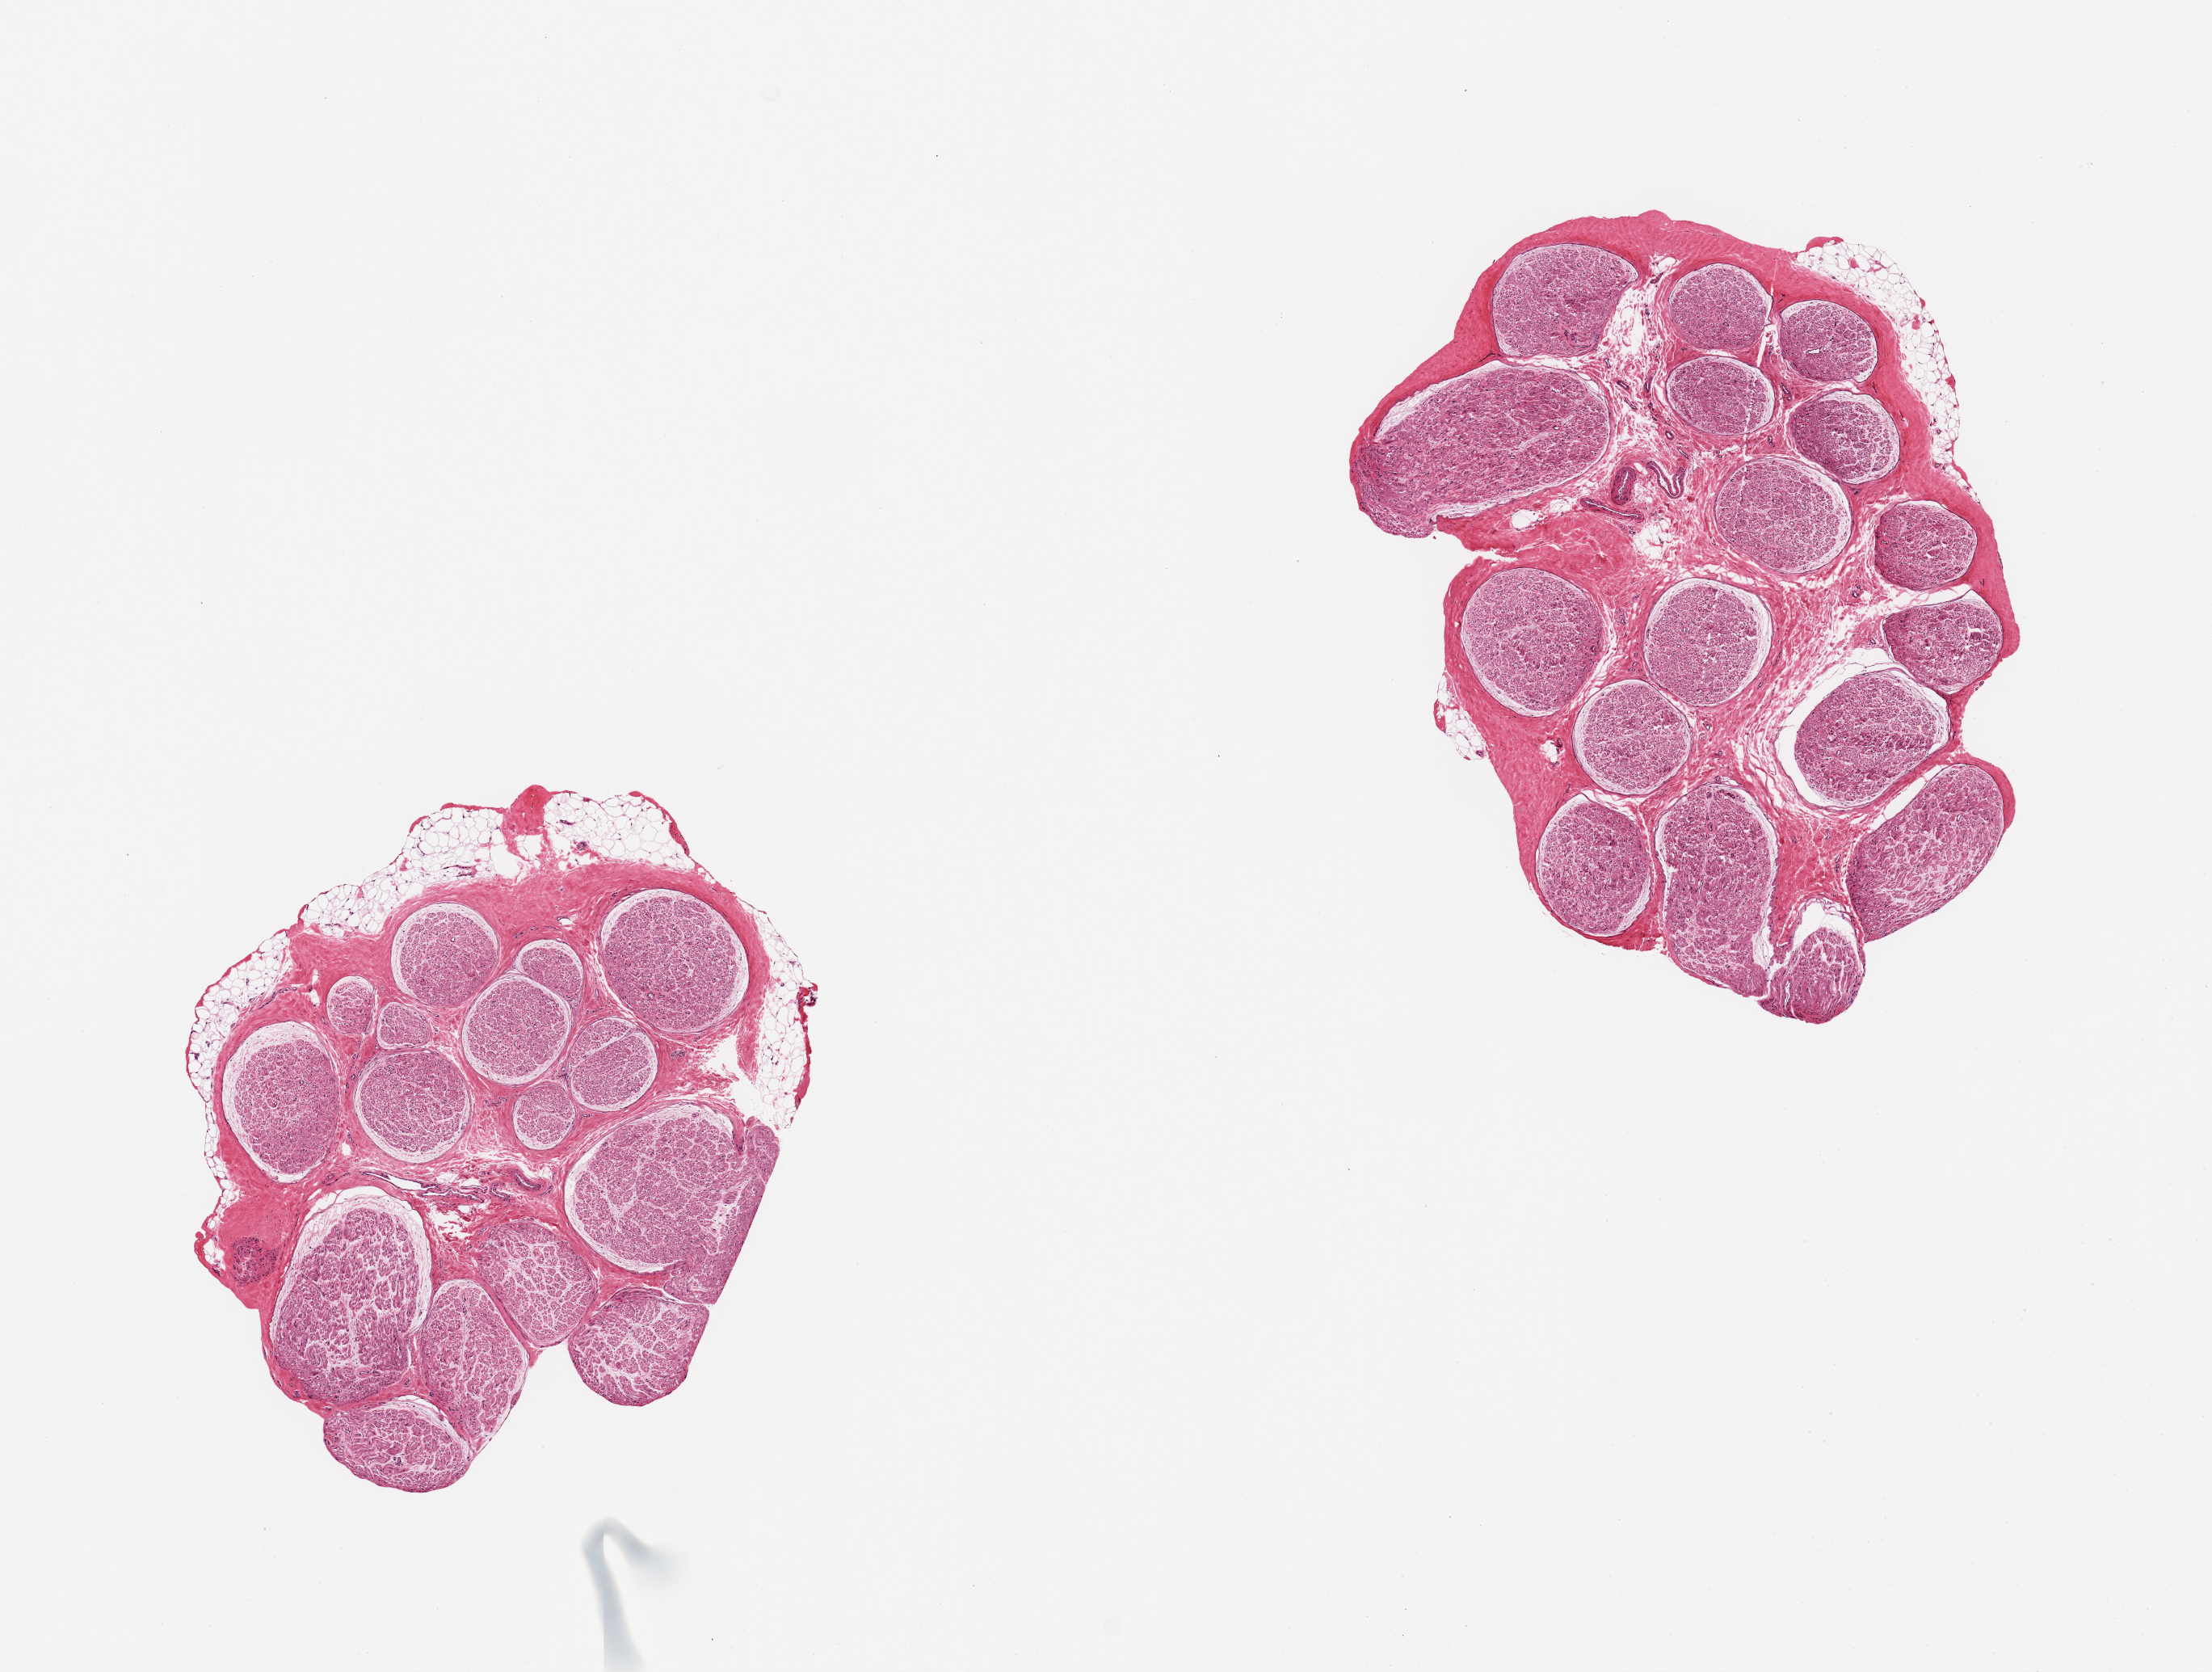
Digitized hematoxylin and eosin (H&E)-stained section, brightfield, a low-resolution overview of the entire scanned area, about 10.8 x 8.2 mm. PAXgene-fixed paraffin-embedded (PFPE) section. Target tissue: tibial nerve. Donor tissue sample.
Pathologist's review note for this sample: 2 pieces; 15% and 5% external fat.